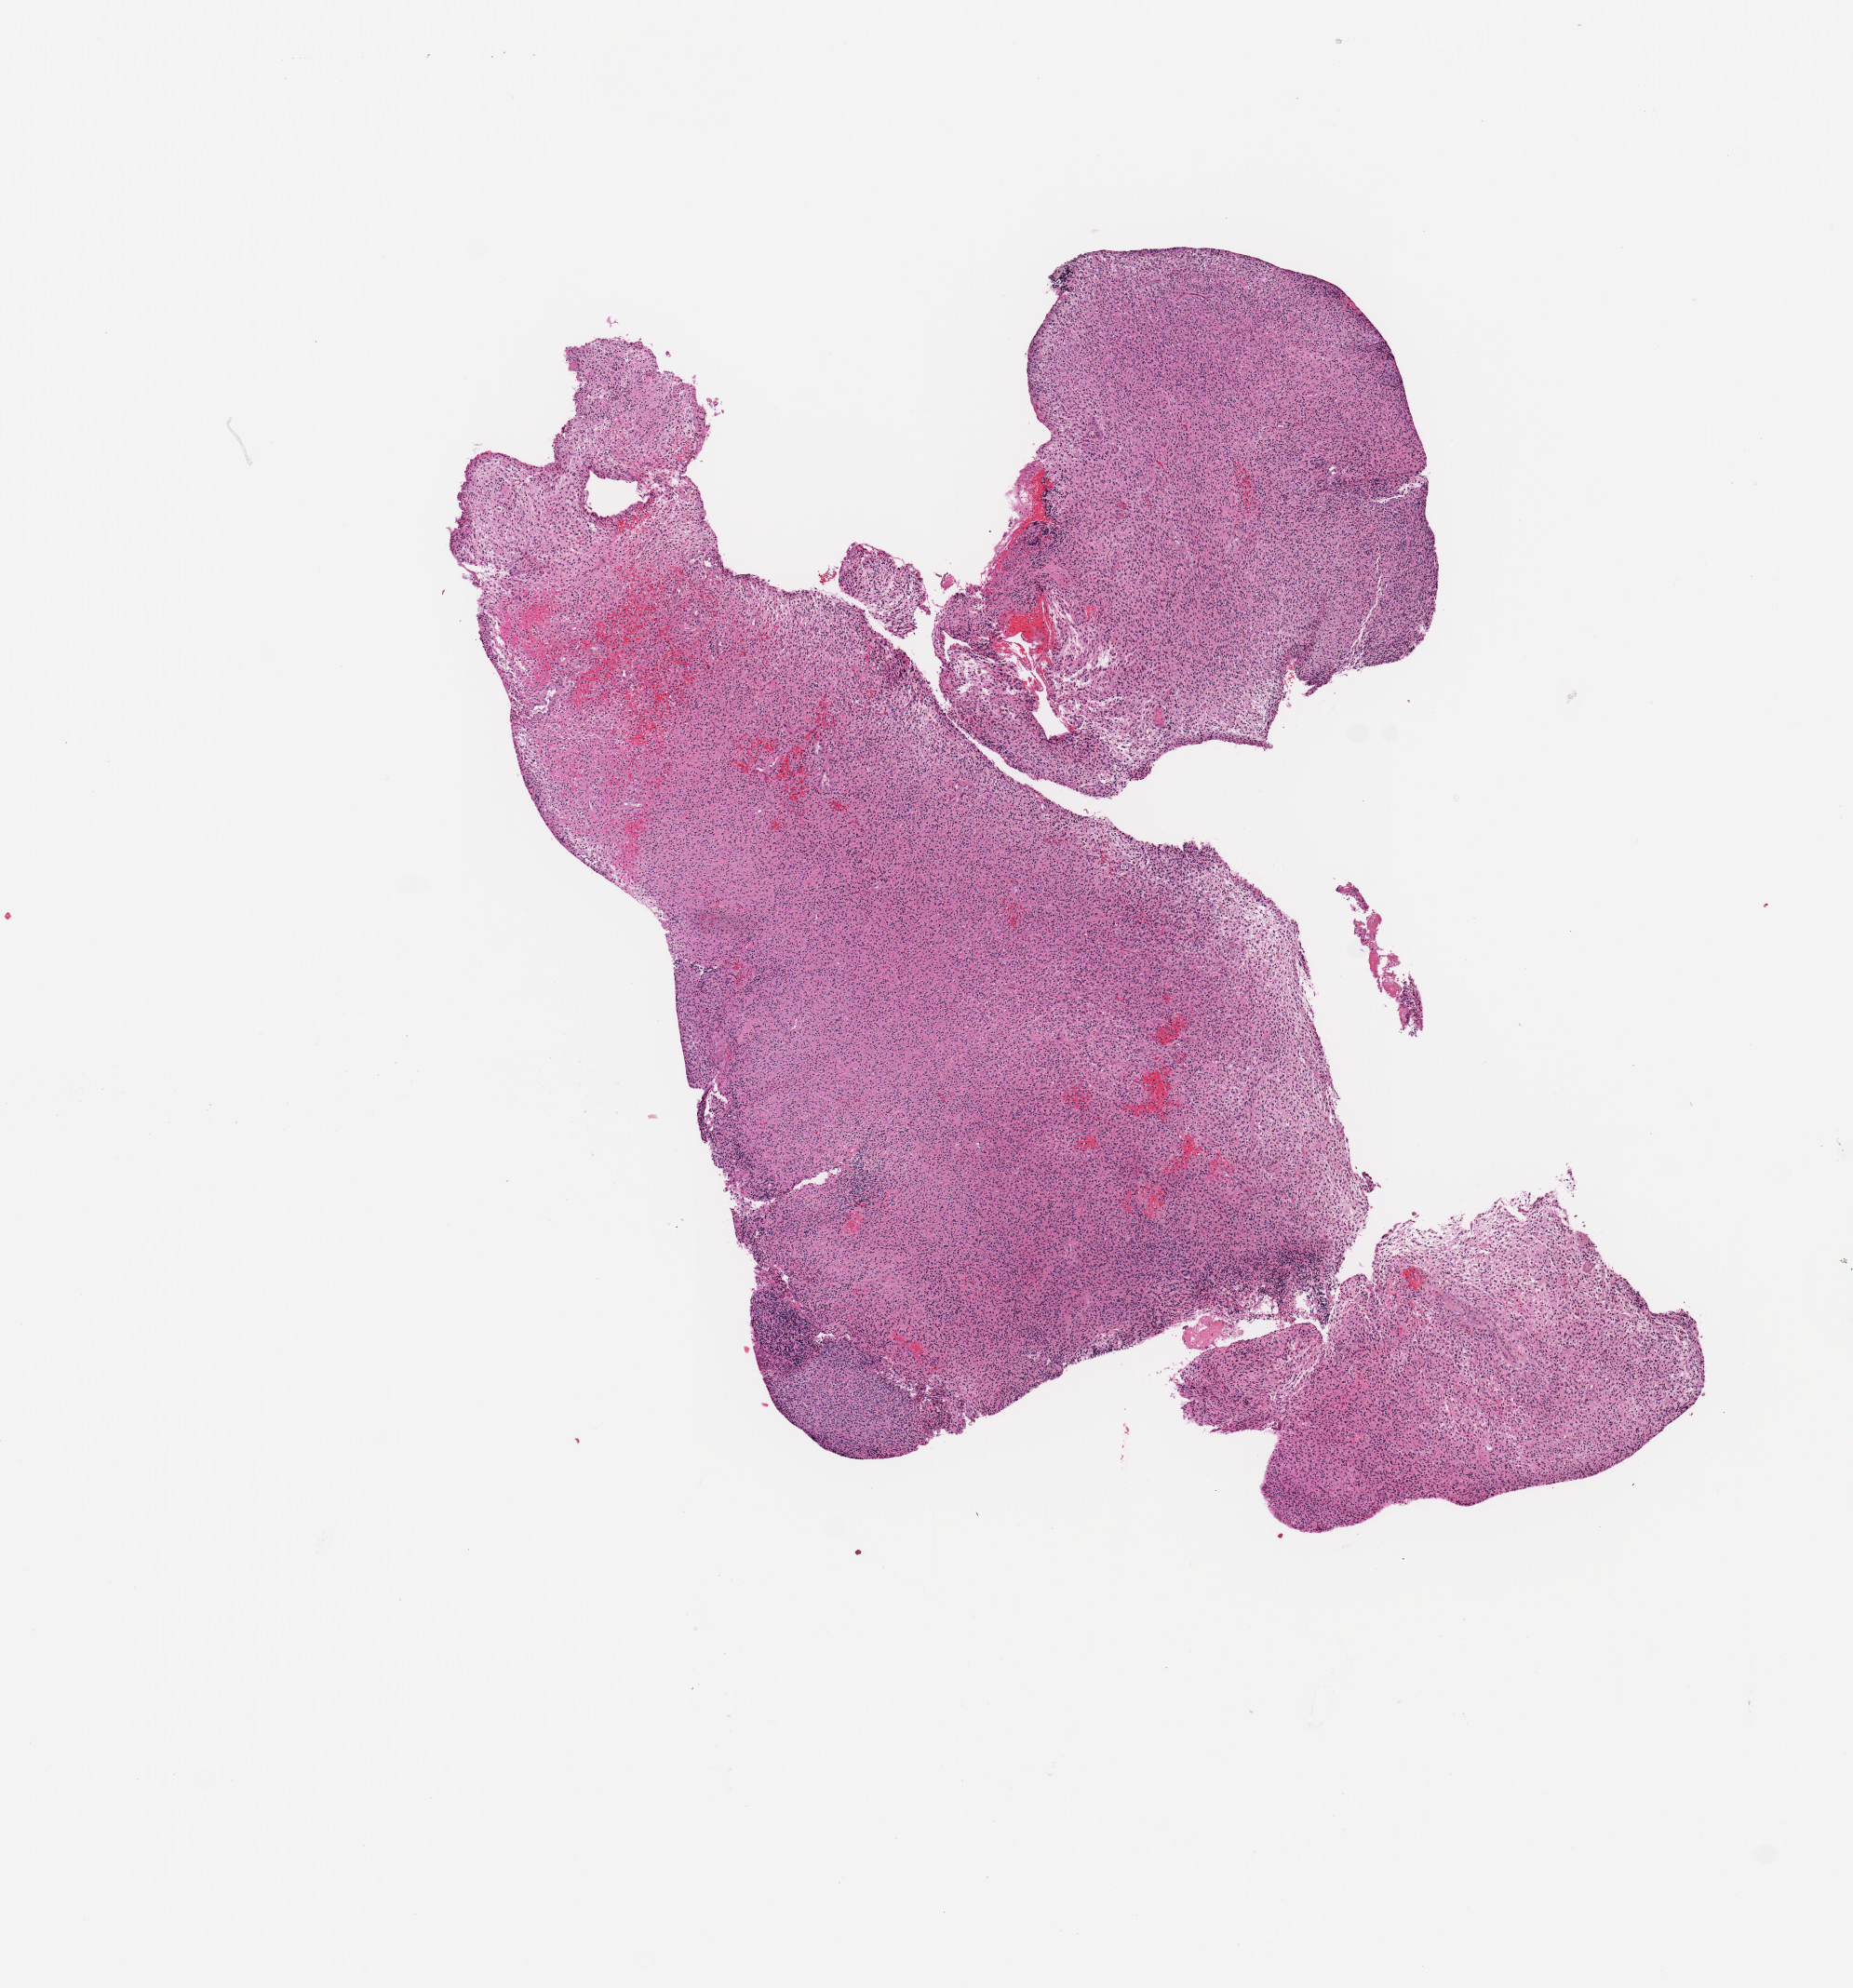
Whole-slide histology image, H&E-stained, low-resolution overview of the scanned area, about 7.9 x 8.4 mm (acquisition: 20x scan). Tumour tissue sample, sampled site: brain. Female, 51 y/o. Composition of this section per pathologist review: tumour nuclei 85%, necrosis 3%.
• histologic diagnosis: Glioblastoma